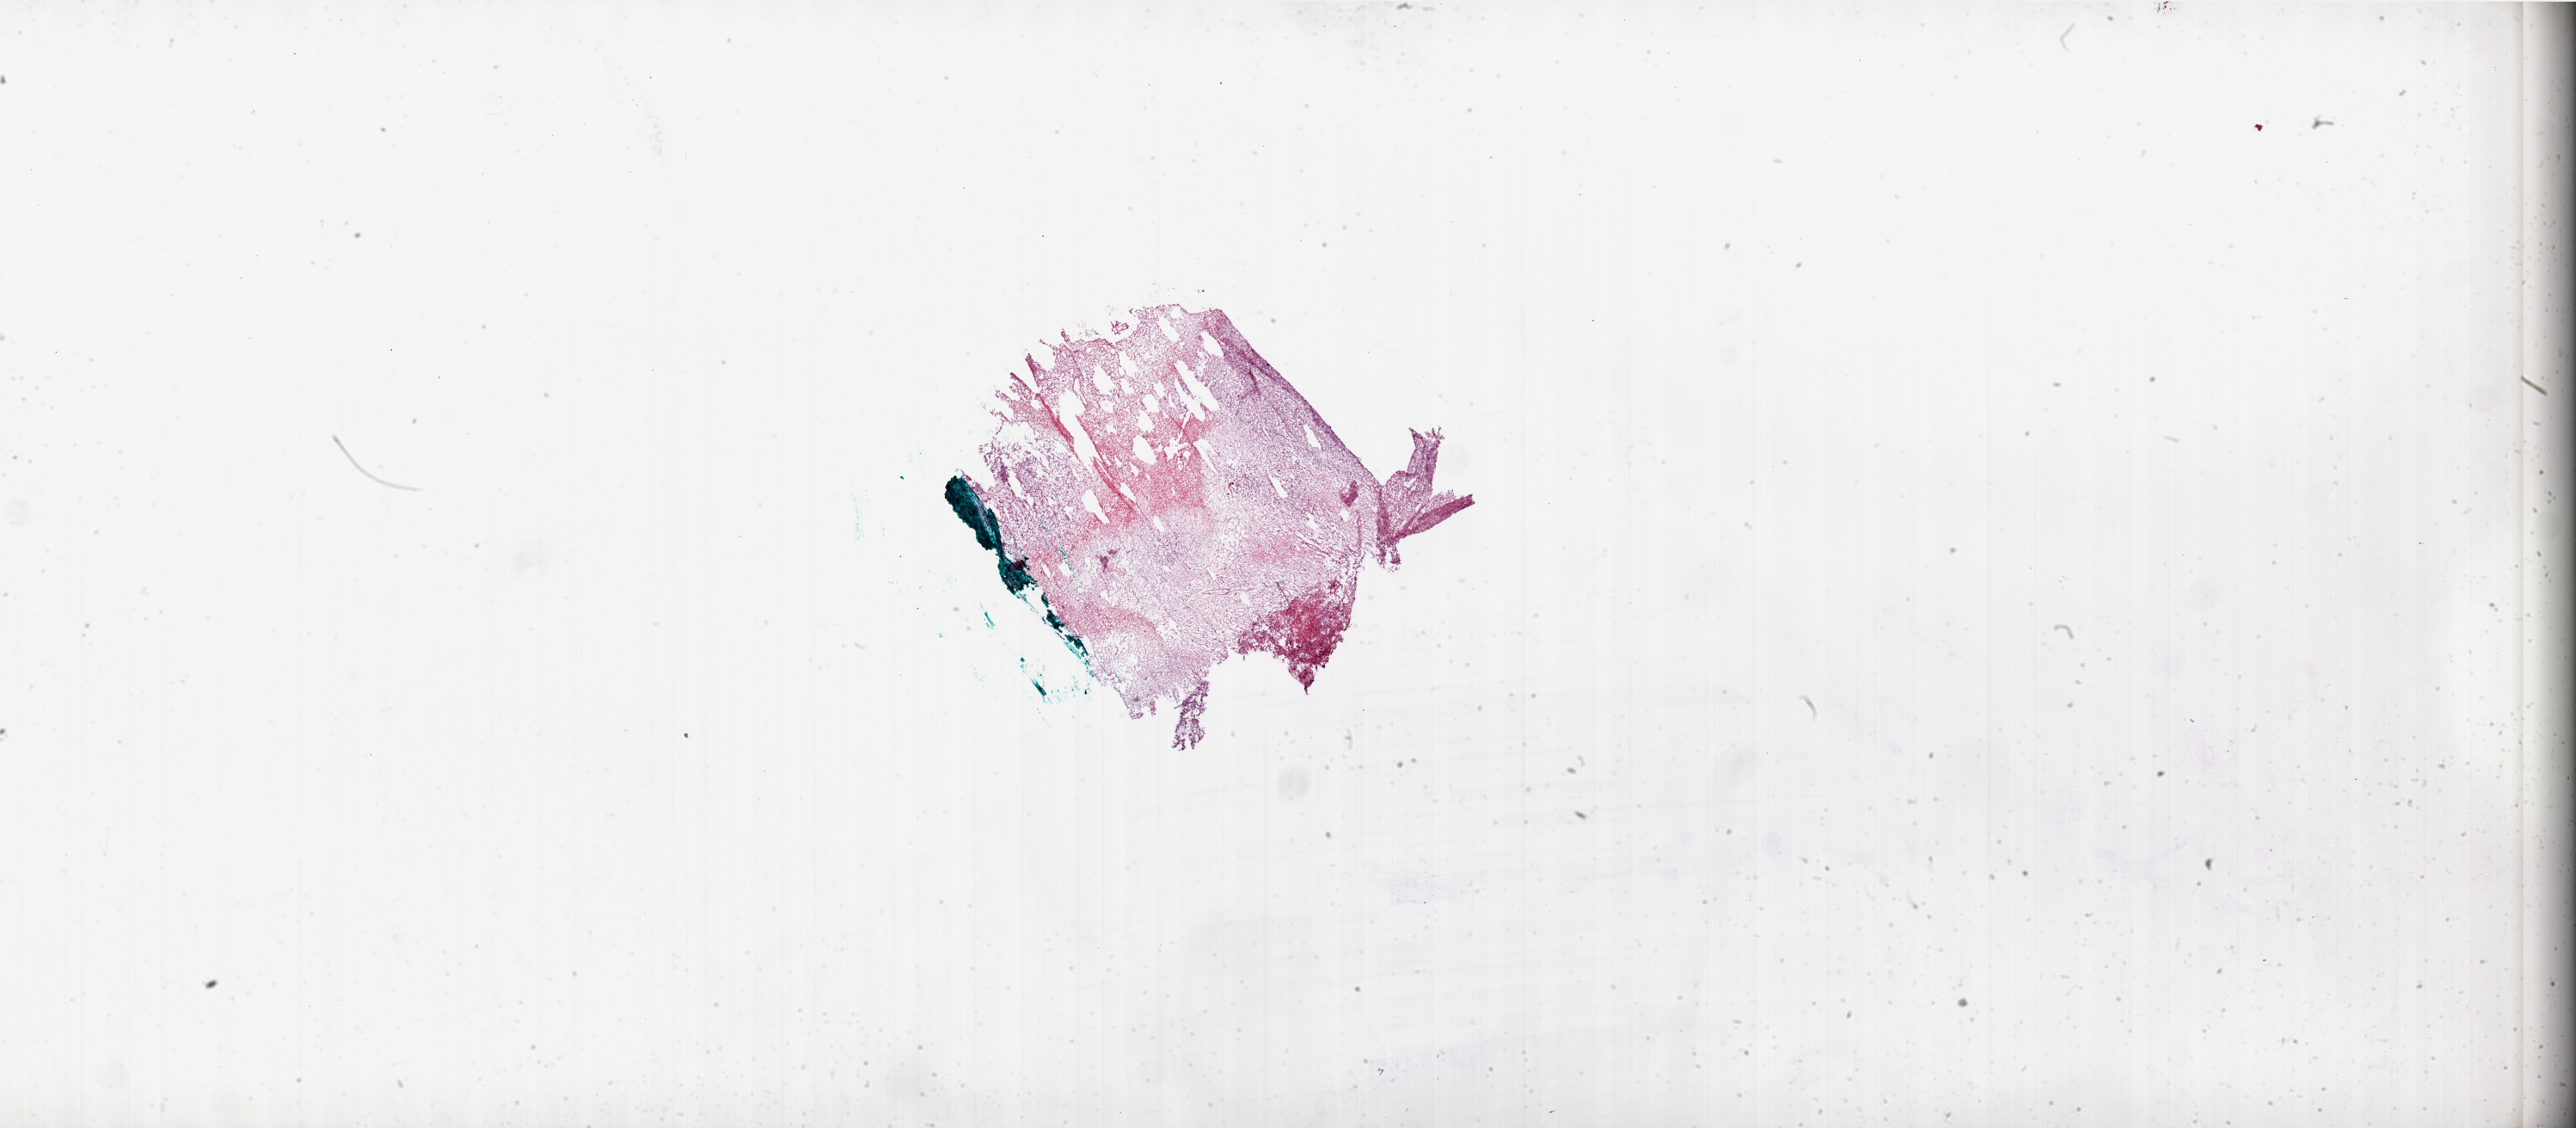
Digitized Hematoxylin and eosin (H&E) stained tissue section (whole slide) — low-resolution overview of the scanned area, about 48.0 x 21.0 mm; frozen section from the bottom of the tissue portion; primary tumour sample from the brain. Male patient; age at initial diagnosis 48 years. Composition of this section per pathologist review: tumour cells 50%, tumour nuclei 100%, normal cells 0%, stromal cells 0%, necrosis 50%.
• diagnosis: Glioblastoma